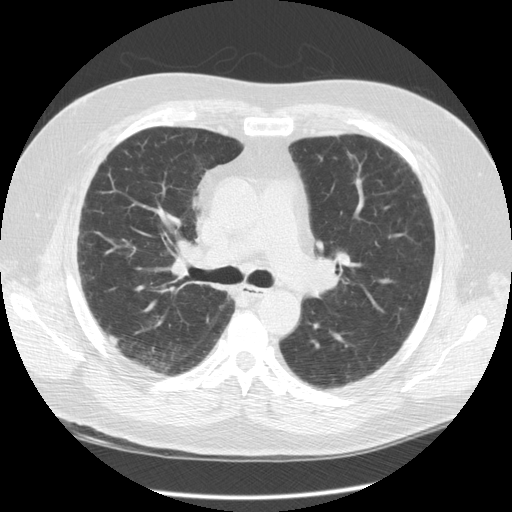
Chest CT (low-dose screening protocol), one axial image. Second annual screen. Lung window (W 1500 / L -600 HU). 120 kVp. 512 × 512 image matrix. Male participant, aged 56 years at enrolment. Current smoker at enrolment.
- Lesion marked by an expert reader, bounding box (x1, y1, x2, y2) in pixels: (98, 322, 131, 355).
- The exam's reader record, not a measurement of the box and not confirmed to be the same lesion: non-calcified nodule or mass ≥4 mm, right upper lobe, 7 × 5 mm, poorly defined margins, soft tissue attenuation, pre-existing on the prior screen: no.
- Lung cancer was diagnosed 399 days after this screen (after the third annual screen): large cell neuroendocrine carcinoma, right upper lobe, stage IIIA (AJCC 6th edition), 10 mm at pathology.